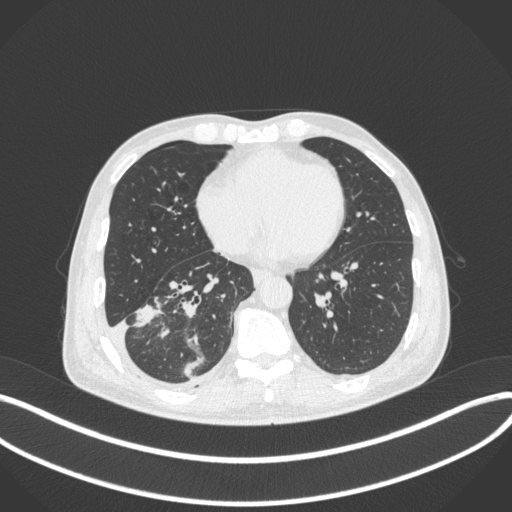
Chest CT, one axial slice; position 145 of 385 along the scan axis; reconstruction kernel B31f; lung window (W 1500 / L -600 HU); 512 × 512 image matrix. Patient: male, 64 years. Case-level facts recorded for this patient, not image findings: clinical TNM (as recorded): T3 N0 M0; histopathological grade: G2-3.
Annotated regions visible in this slice (rectangle marked by the reading radiologist):
- lung tumour (recorded histology: adenocarcinoma): bounding box [x1, y1, x2, y2] px = [132, 301, 167, 334]